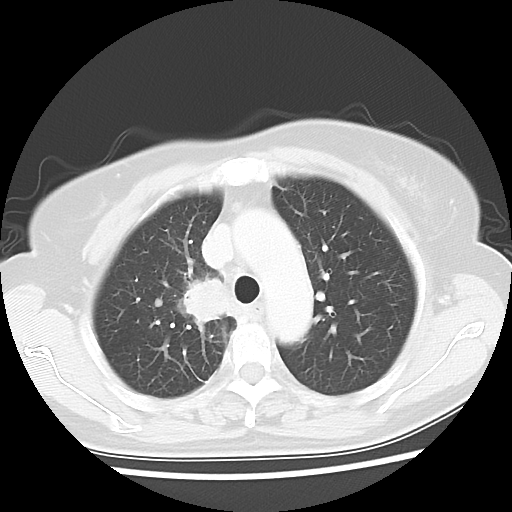
Chest CT, one axial slice. Slice 42 of 56 in the series (ordered by position). Reconstruction kernel LUNG. Lung window (W 1500 / L -600 HU). 512 × 512 image matrix. Female patient, age 62 years. From the clinical record (not read from this slice): clinical TNM (as recorded): T2 N1 M1a.
Structures marked on this image (bounding box drawn by a radiologist):
- lung tumour (recorded histology: adenocarcinoma): box from (x=177, y=272) to (x=248, y=335) px